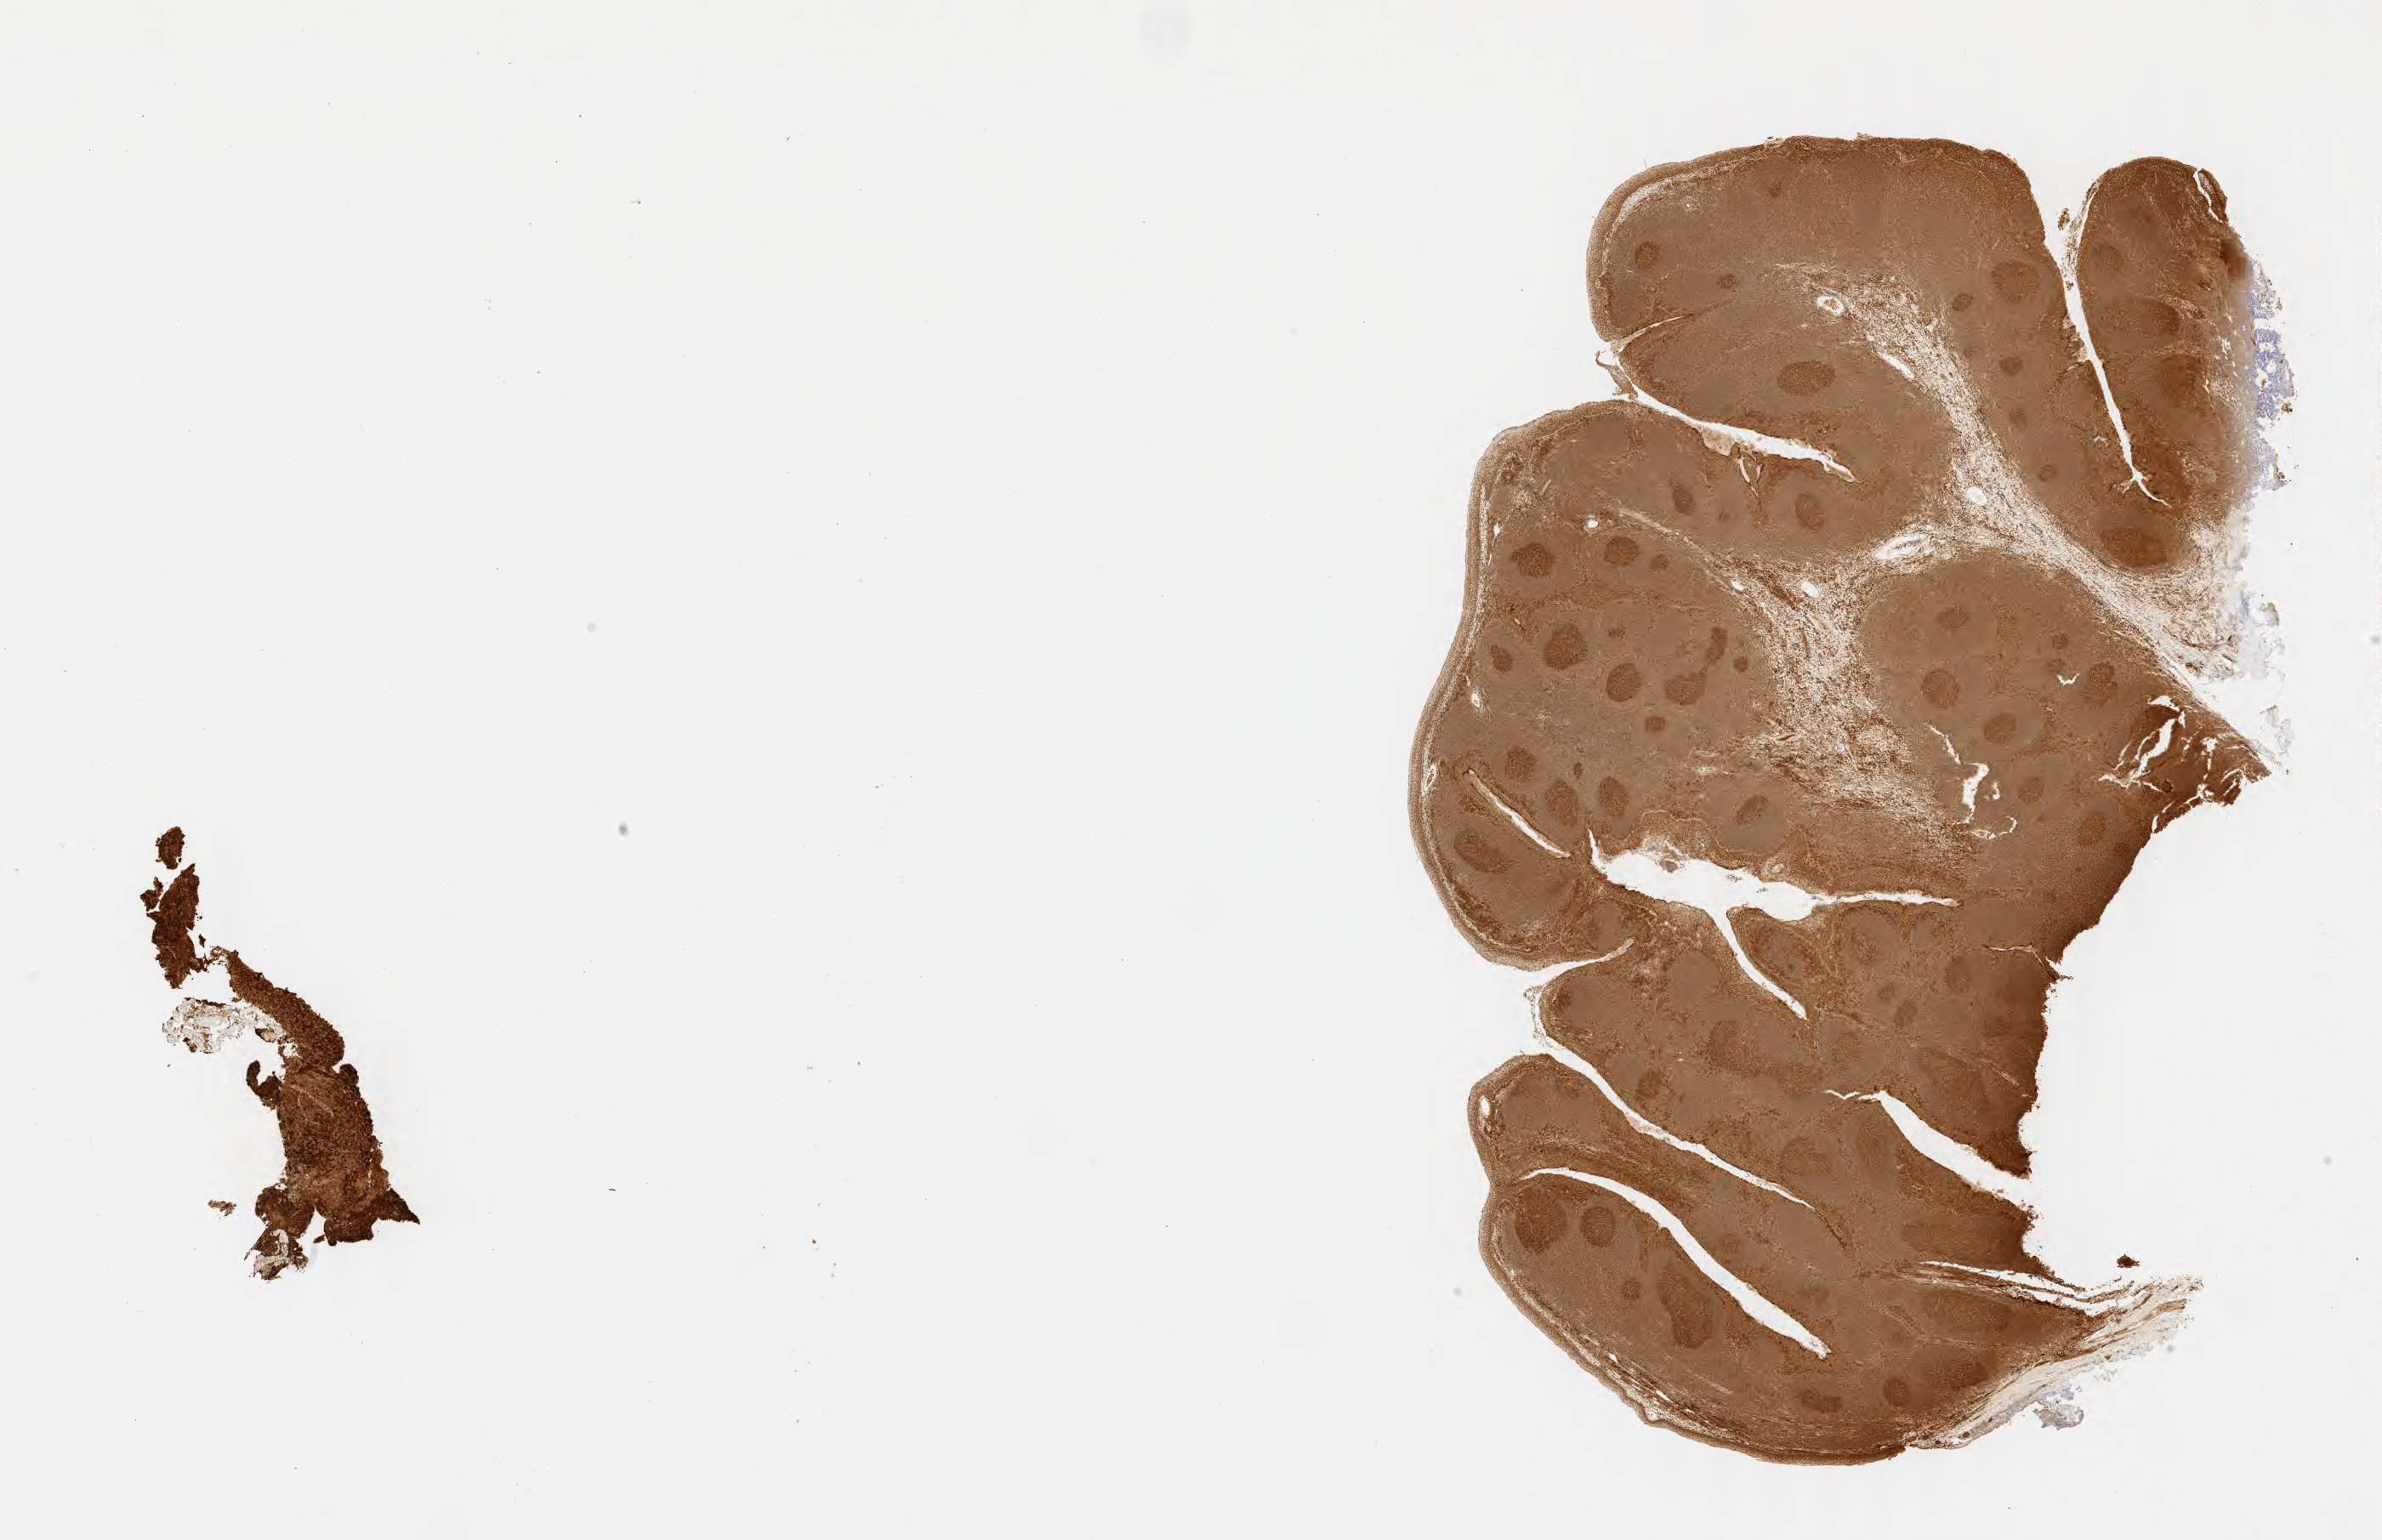
IHC for BCL6, whole-slide image, low-resolution overview of the scanned area, about 22.6 x 14.6 mm, tumor tissue. Female patient, 27 years old.
Histologic diagnosis: Diffuse large B-cell lymphoma, NOS.